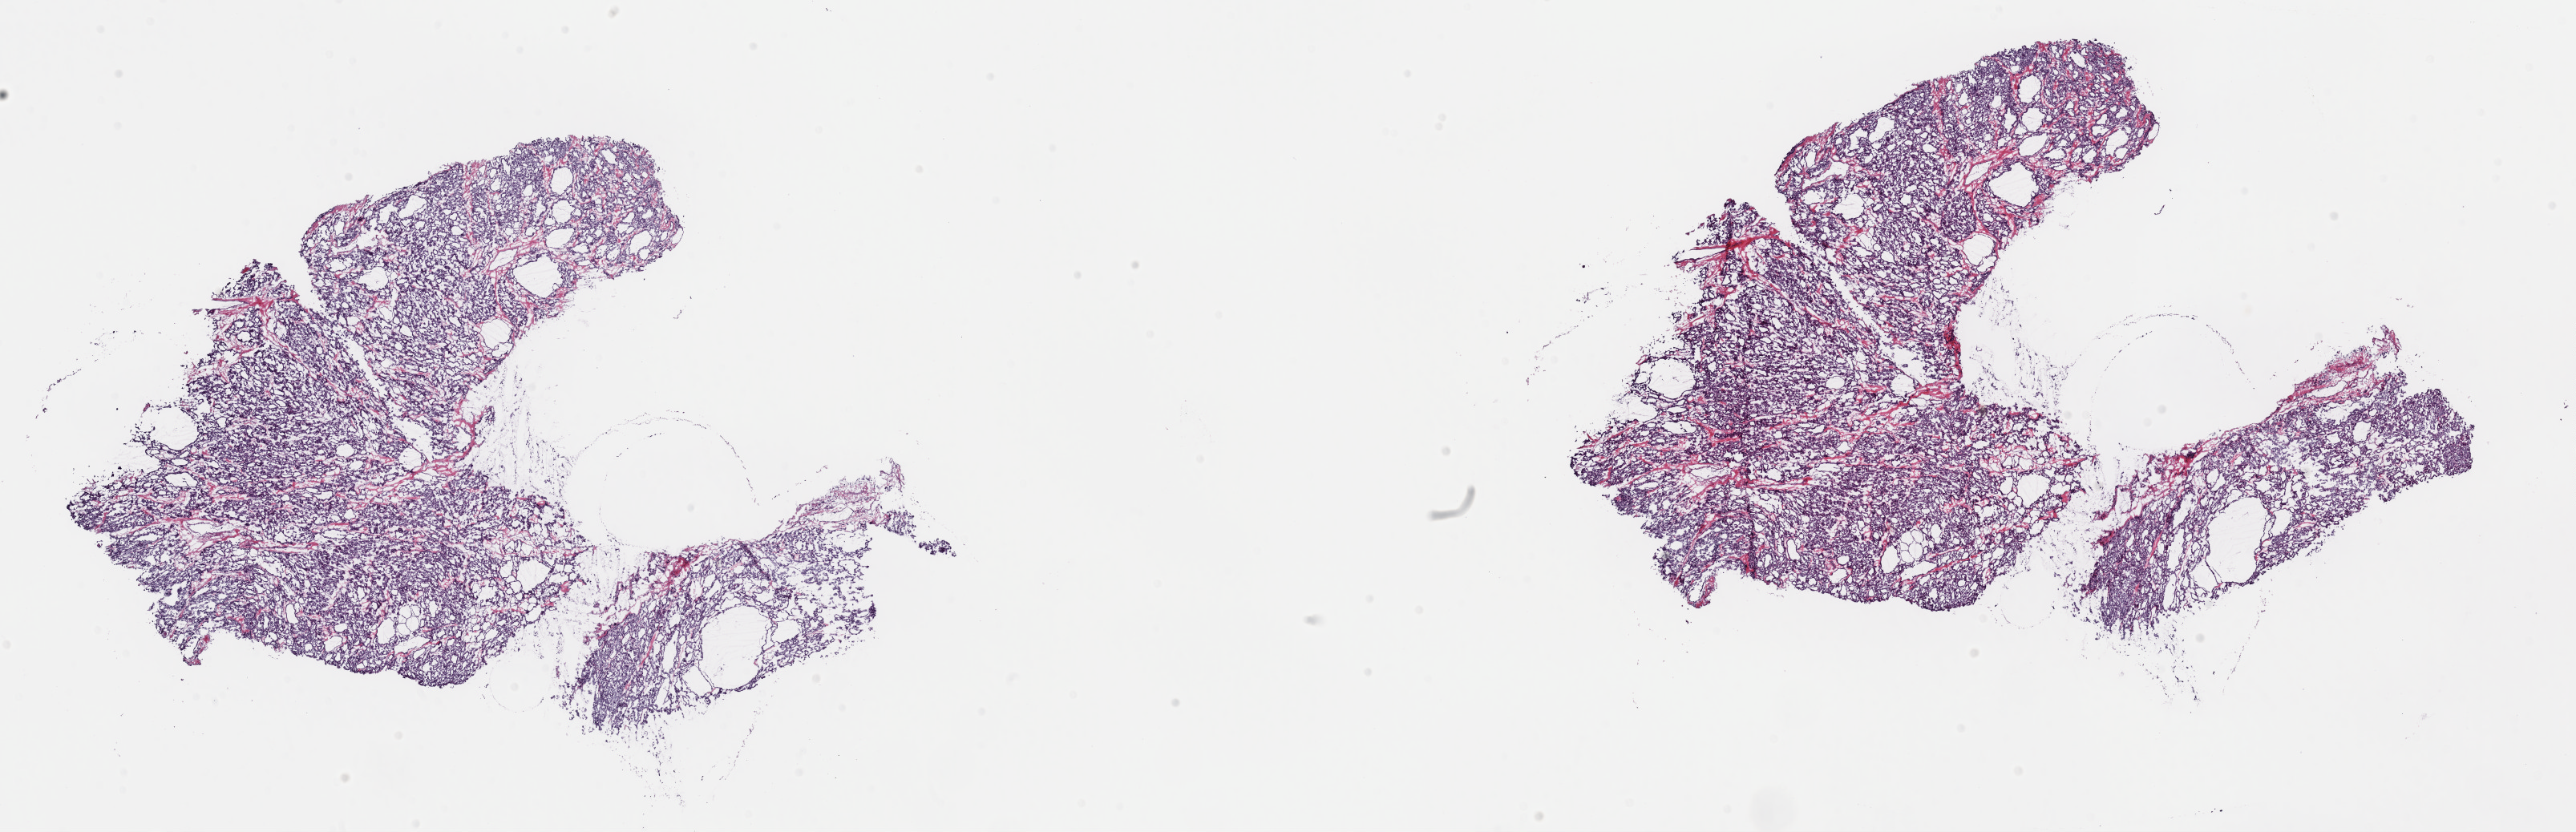
Whole-slide histology image, Hematoxylin and eosin (H&E) stained, shown as a low-resolution overview of the whole scanned area (about 25.4 x 8.2 mm); frozen section from the top of the tissue portion; thyroid, primary tumour sample. Male patient; age at initial diagnosis 58 years. Pathologist review of this section (percent, as recorded): tumour cells 95%, tumour nuclei 95%, normal cells 0%, stromal cells 5%, necrosis 0%. Inflammatory infiltration, as recorded: lymphocyte infiltration 0%, monocyte infiltration 0%, neutrophil infiltration 0%.
Histologic diagnosis: Papillary adenocarcinoma, NOS. TNM: T2 N0 MX. AJCC pathologic stage: II (5th edition).